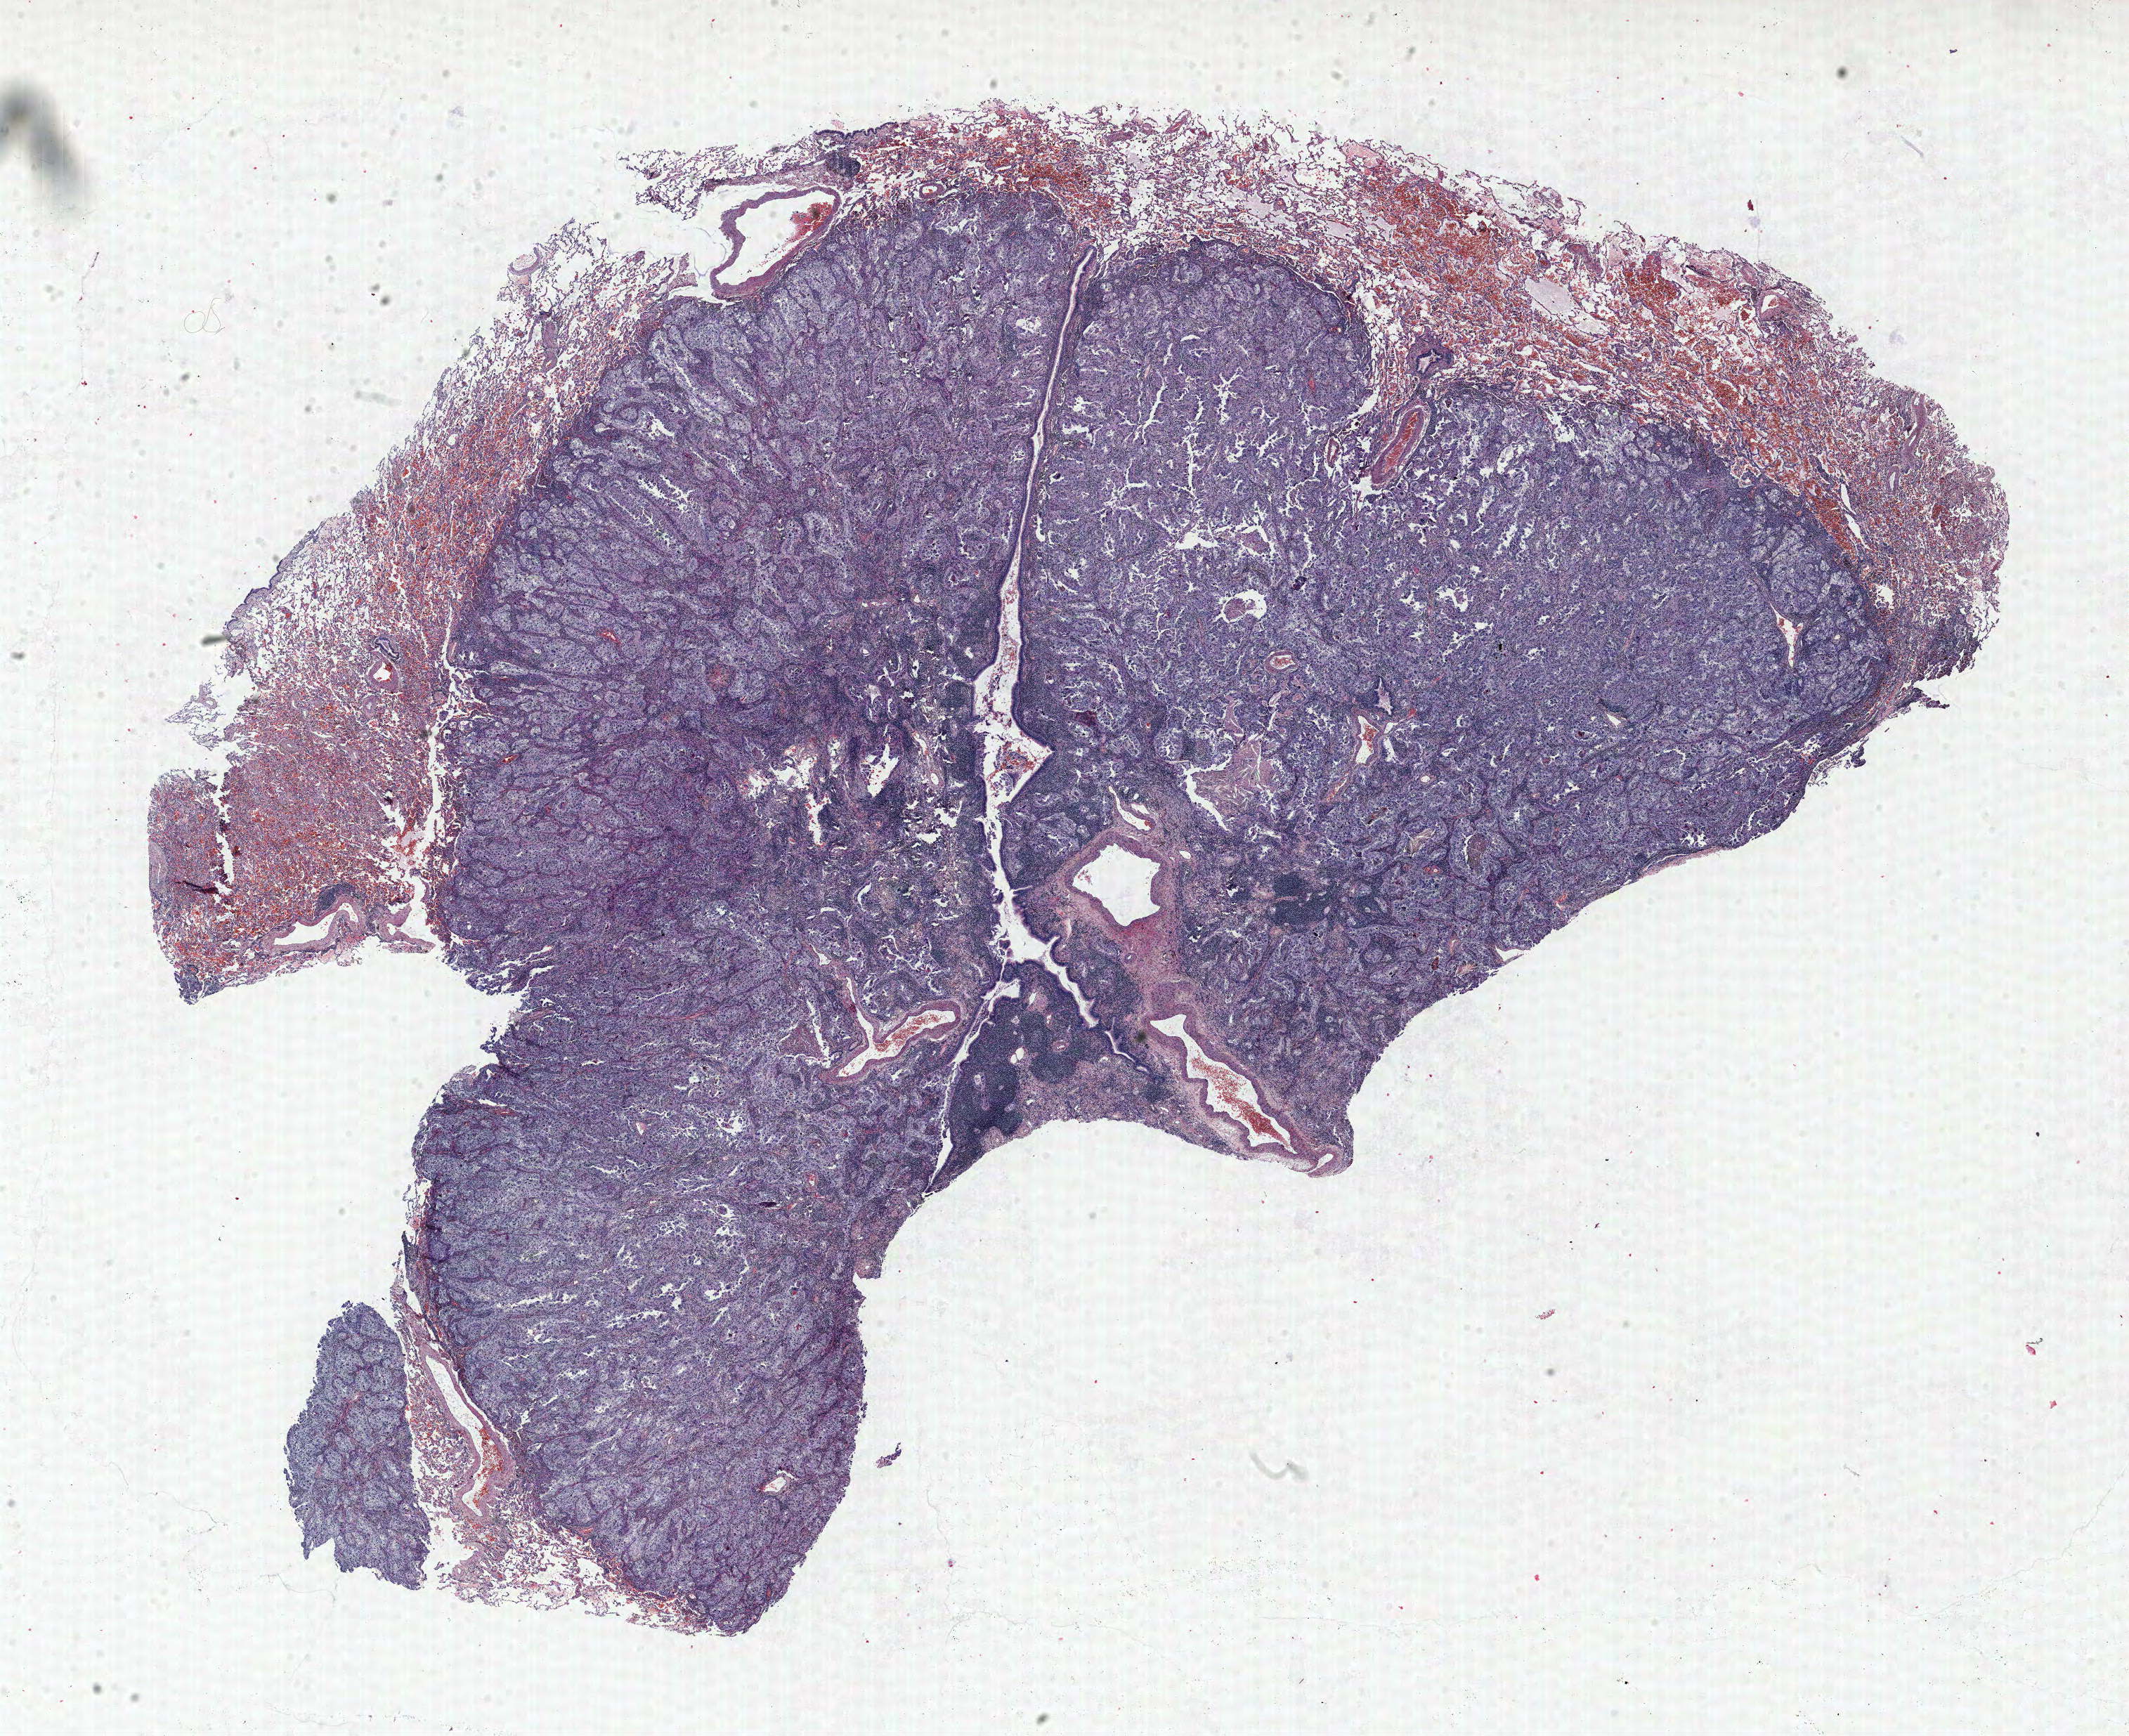
Whole-slide histology image, Hematoxylin and eosin (H&E) stained, whole scanned area (about 24.2 x 19.8 mm, acquisition: 40x scan) shown as a low-resolution overview; FFPE section; lung tissue. Male patient, aged 57 at enrolment. Grade: poorly differentiated (G3).
• primary tumour location (clinical record): right lower lobe
• ICD-O-3 topography: lower lobe of lung (C34.3)
• stage (AJCC 6th edition): IA
• participant's lung-cancer diagnosis: Adenocarcinoma, NOS (ICD-O-3 8140/3)
• tumour size (pathology): 24 mm